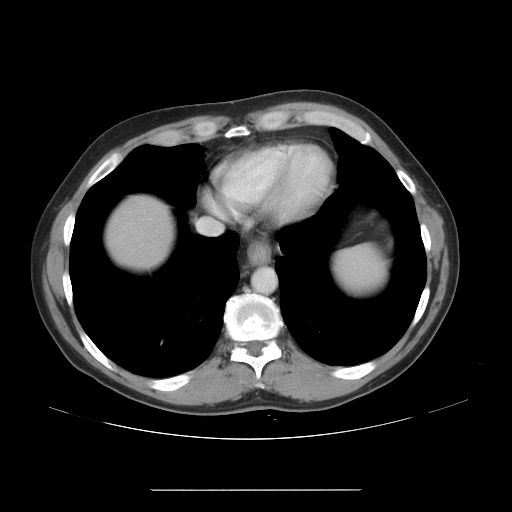
Contrast-enhanced abdominal CT, one axial slice; position 41 of 48 along the scan axis; 120 kVp; soft-tissue window (W 400 / L 40 HU); 5 mm slice thickness; 512 × 512 image matrix, field of view 409 × 409 mm. Male patient, age 56 years. Case-level facts recorded for this patient, not image findings: diagnosis: colorectal cancer liver metastases, imaged before liver resection.
Annotated regions visible in this slice (expert manual segmentation):
- hepatic veins: bounding box <197,220,222,235> (left, top, right, bottom; pixels)
- liver: <111,200,169,264>
- planned liver remnant (the part of the liver to remain after resection): <111,200,169,264>